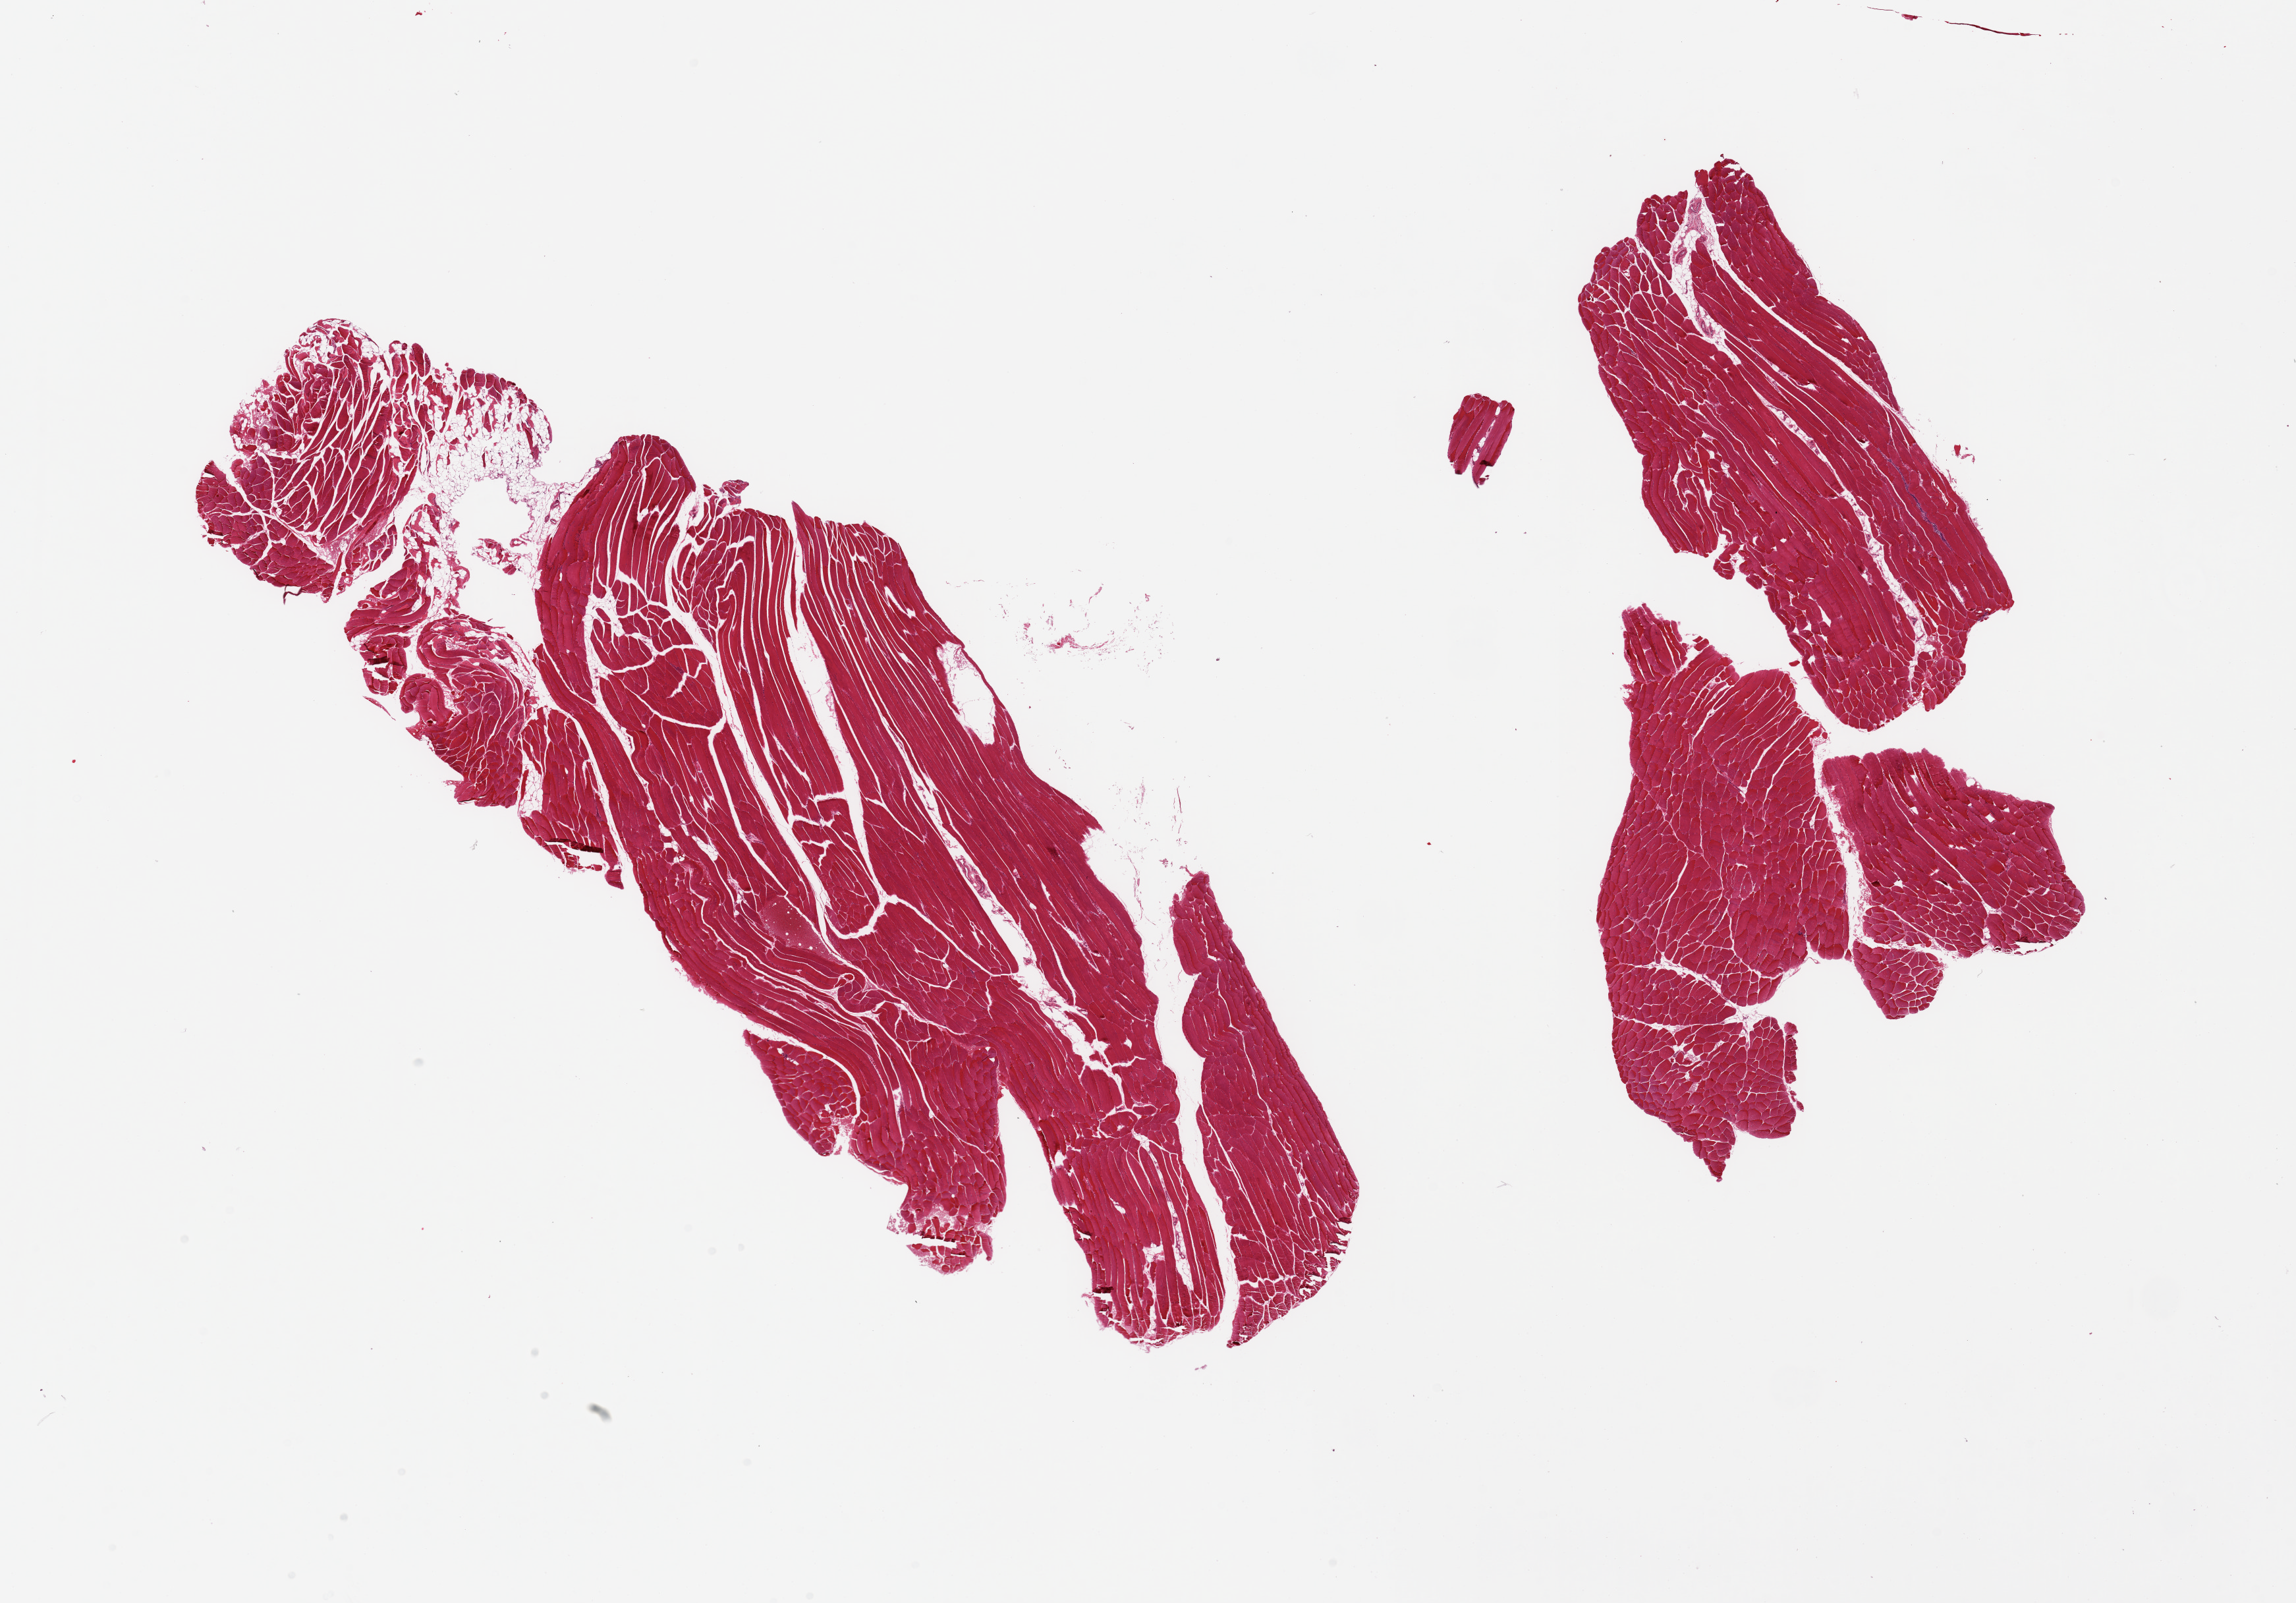
Whole-slide image, H&E stain, whole scanned area (about 27.6 x 19.2 mm, from a 20x scan) shown as a low-resolution overview. PAXgene-fixed, paraffin-embedded tissue. Target tissue: skeletal muscle. Tissue donor sample. Donor: male.
Pathologist's review note for this sample: 2 pieces. Skeletal muscle (not mammary tissue).